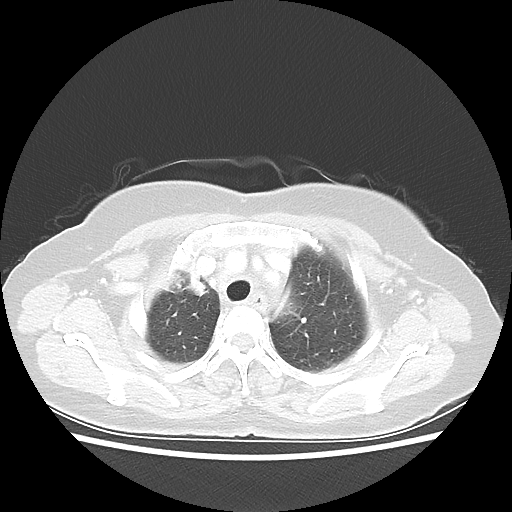
Chest CT, one axial slice. Position 44 of 55 along the scan axis. Reconstruction kernel LUNG. 80 kVp. Lung window (W 1500 / L -600 HU). 512 × 512 image matrix, field of view 337 × 337 mm. Female patient, age 62 years. From the clinical record (not read from this slice): clinical TNM (as recorded): T4 N3 M0.
Structures marked on this image (rectangle marked by the reading radiologist):
- lung tumour (recorded histology: squamous cell carcinoma): box from (x=157, y=254) to (x=216, y=303) px